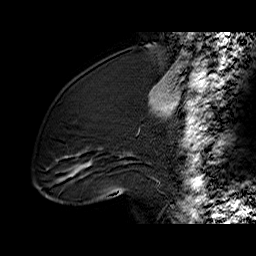
Breast MRI (dynamic contrast-enhanced), one sagittal slice. Position 24 of 60 along the scan axis. Dynamic contrast-enhanced series, time point 2 of 6 at this slice position (early post-contrast). 1.5 T. TE 6.2 ms, TR 32.4 ms. 4 mm slice thickness. 256 × 256 image matrix, field of view 200 × 200 mm. Female patient. Case-level facts recorded for this patient, not image findings: setting: breast cancer imaged before/during neoadjuvant chemotherapy; receptor status: triple-negative.
Annotated regions visible in this slice (semi-automatic segmentation, software-assisted and operator-edited):
- analysis volume of interest (the breast-tissue region the enhancement analysis was run in; not a lesion): bounding box [x1, y1, x2, y2] px = [36, 99, 134, 196]
- tumour enhancement mask (voxels above the 100 % enhancement threshold inside the analysis volume of interest): [73, 174, 75, 176]